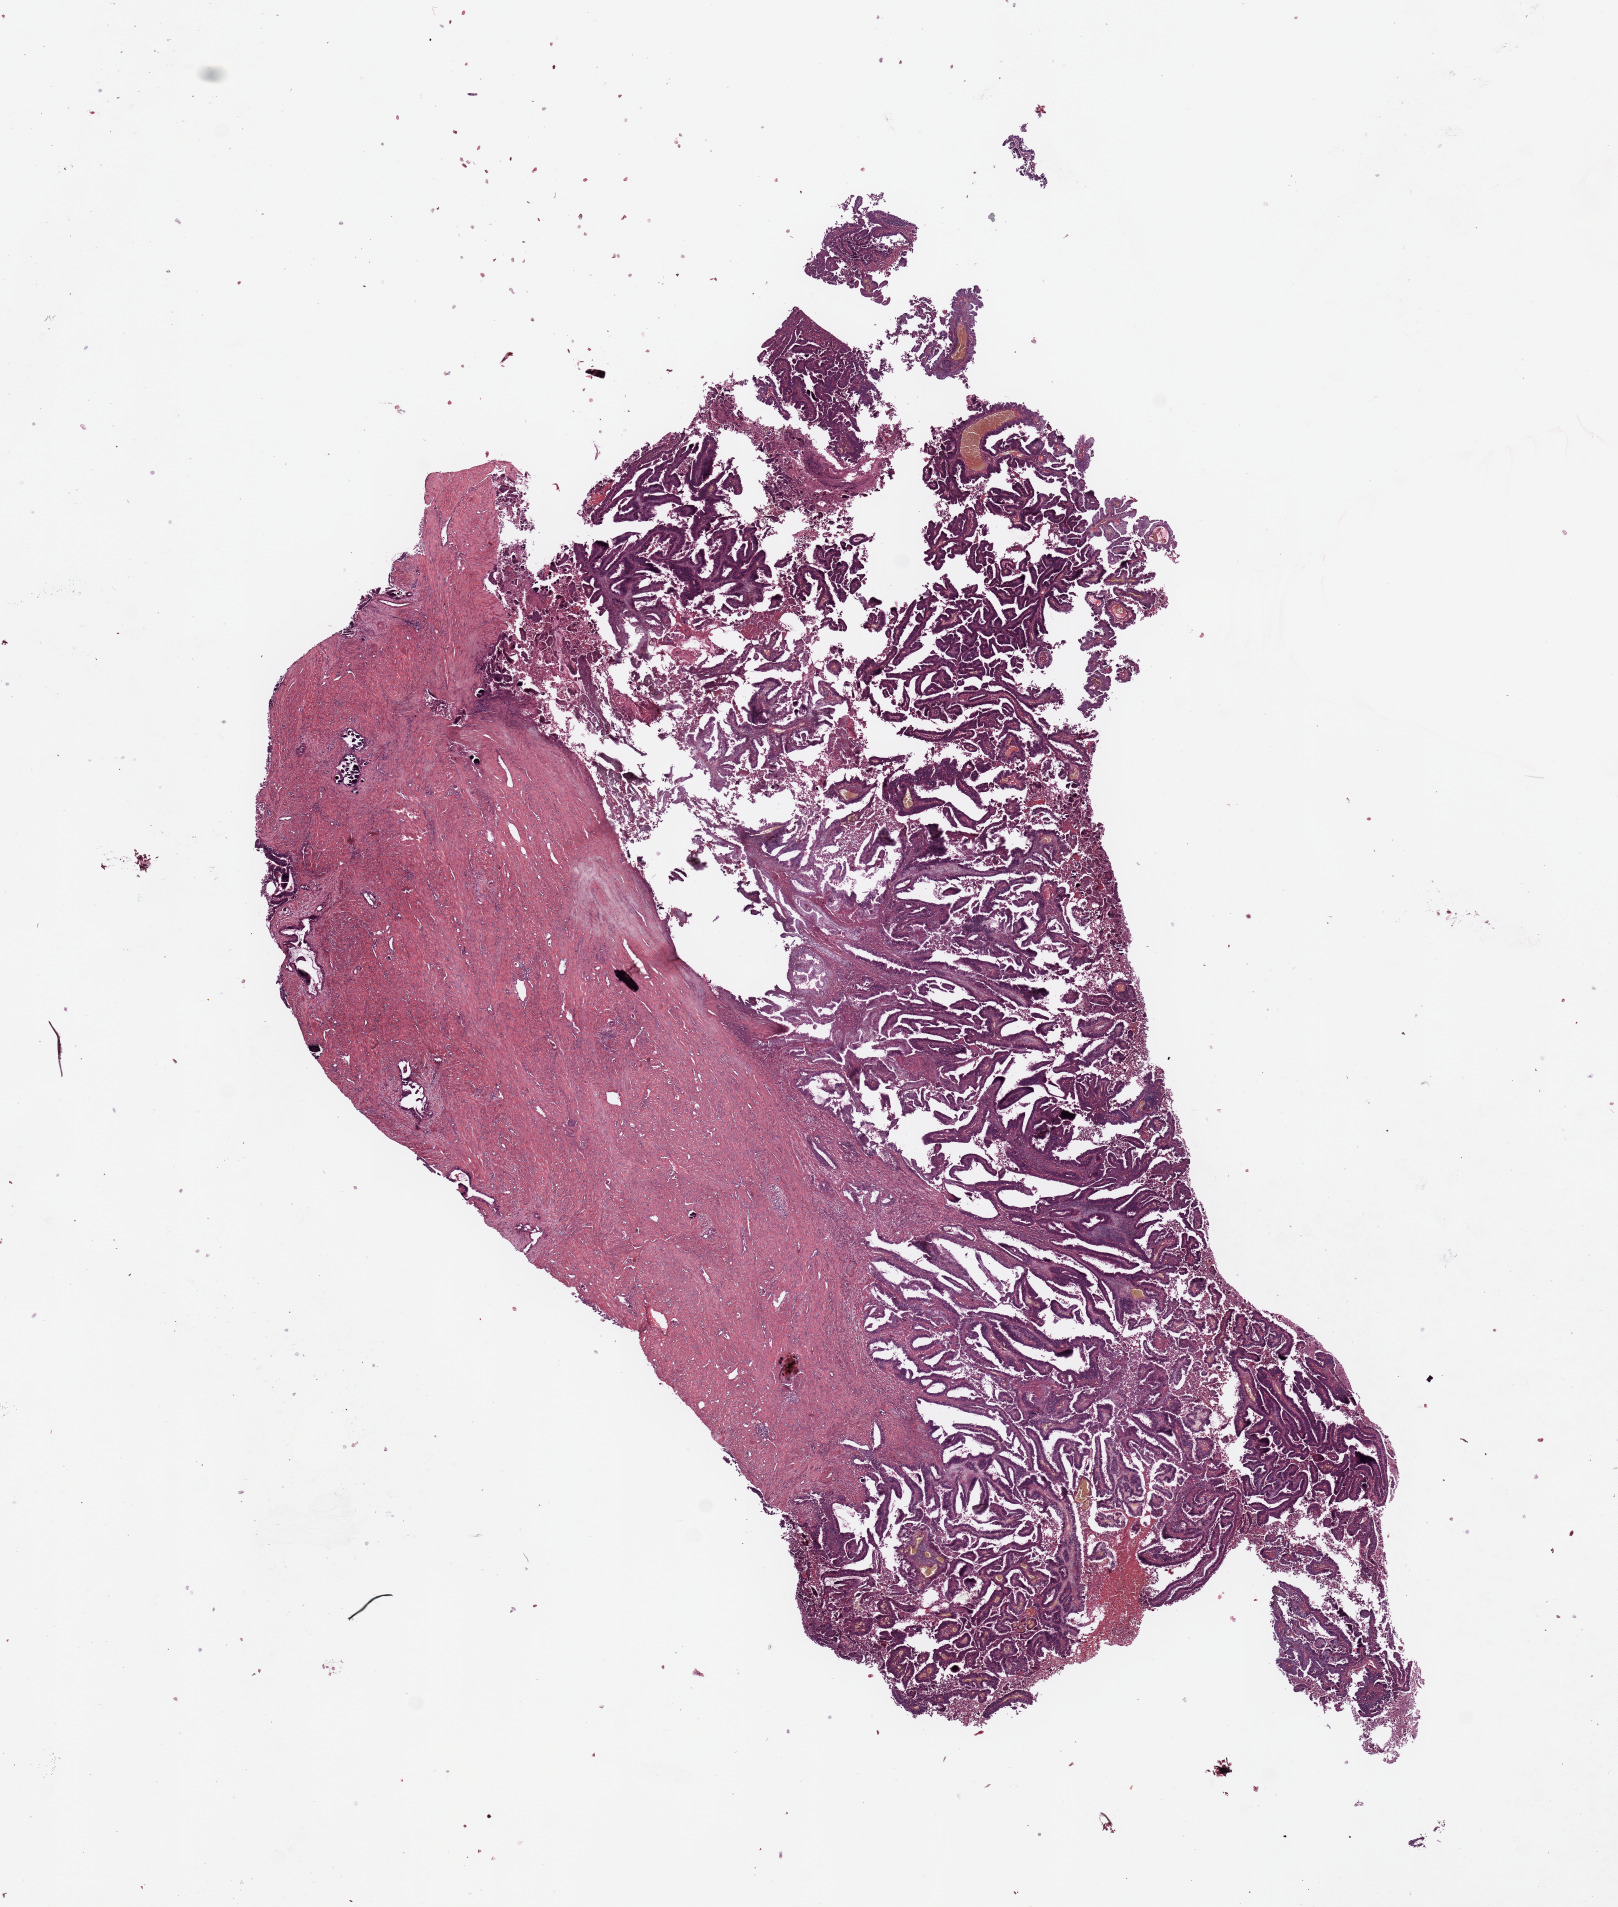
Hematoxylin and eosin (H&E) stained whole-slide image — low-resolution overview of the scanned area, about 12.8 x 15.1 mm (slide scanned at 20x), uterus, tumour tissue. Female, 70 y/o. Histologic grade: G3 (poorly differentiated).
AJCC pathologic stage: I. Diagnosis: Endometrioid adenocarcinoma, NOS.